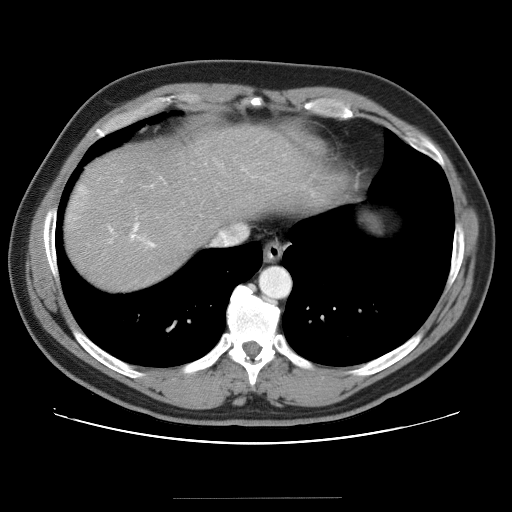
Contrast-enhanced abdominal CT (liver protocol), one axial slice; position 33 of 40 along the scan axis; reconstruction kernel STANDARD; 120 kVp; soft-tissue window (W 400 / L 40 HU); 512 × 512 image matrix. From the clinical record (not read from this slice): diagnosis: hepatocellular carcinoma (patient treated with transarterial chemoembolisation; whether this scan precedes or follows treatment is not stated here); TNM stage (as recorded): Stage-IVA; Child-Pugh class: B; tumour nodularity: multinodular.
Outlined on this slice (semi-automatically segmented with operator editing):
- abdominal aorta: bounding box <260,267,290,297> (left, top, right, bottom; pixels)
- liver parenchyma outside the tumour (the mass and vessels are separate outlines, so this box may not span the whole liver): <64,124,382,290>
- mass: <68,186,87,223>
- liver vessels: <111,223,155,247>